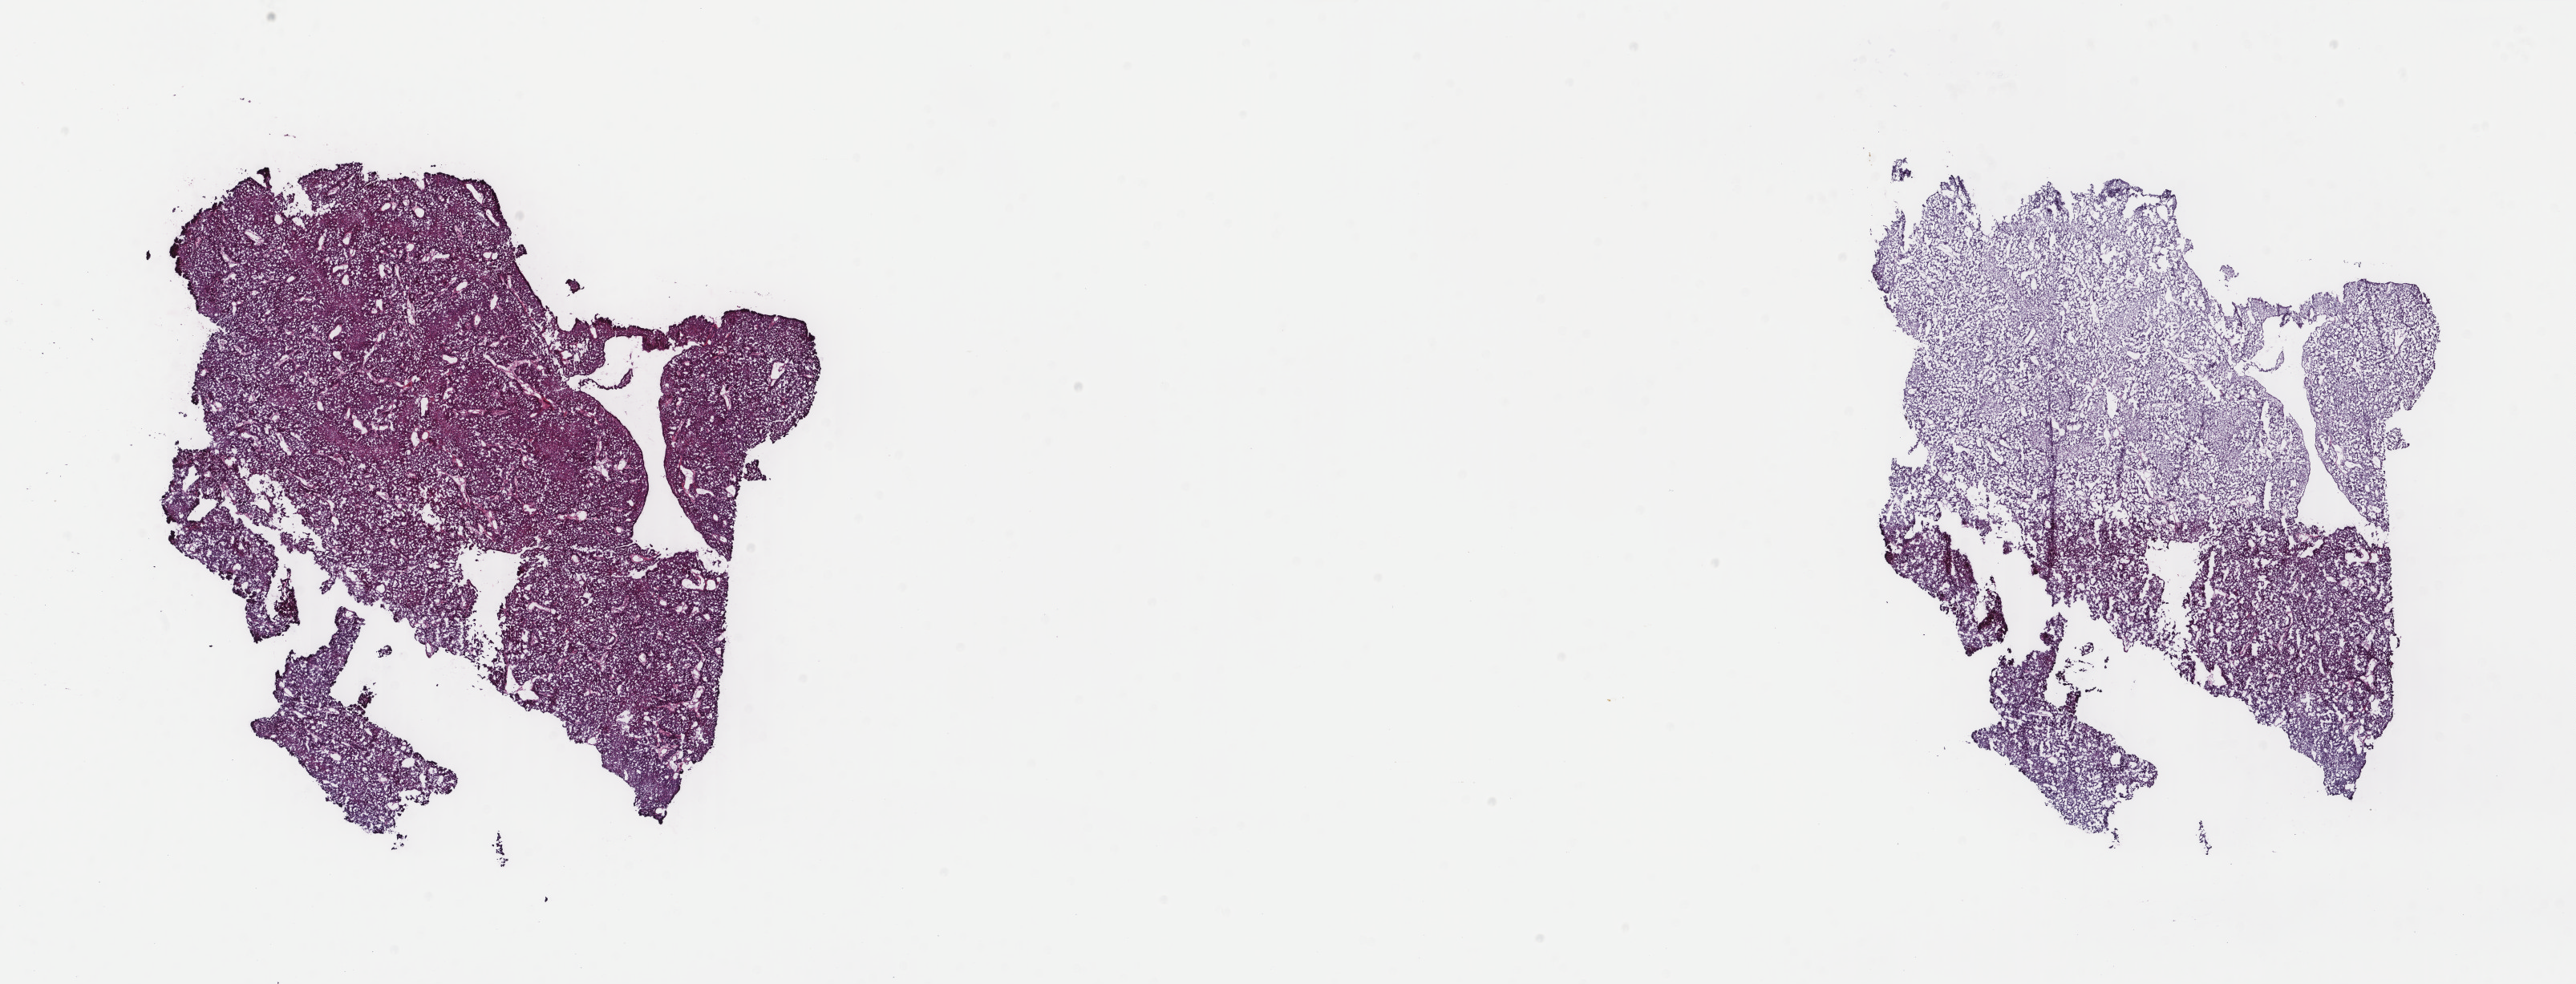
Whole-slide histology image, H&E — low-resolution overview of the scanned area, about 25.5 x 9.7 mm (from a 40x scan); frozen section from the bottom of the tissue portion; breast, primary tumour sample. Female patient; age at initial diagnosis 72 years. Slide review estimates, as recorded: tumour cells 96%, tumour nuclei 96%, normal cells 0%, stromal cells 4%, necrosis 0%. Infiltration values recorded for this section: lymphocyte infiltration 1%, monocyte infiltration 0%, neutrophil infiltration 0%.
• lymph nodes positive (case pathology): 0 of 5 examined
• AJCC pathologic stage: IIA
• histologic diagnosis: Papillary carcinoma, NOS